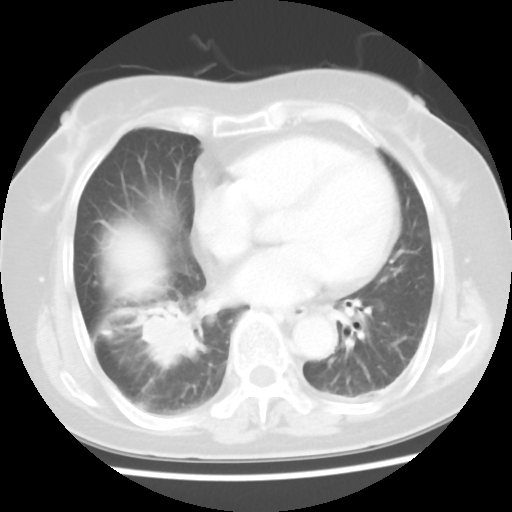
Chest CT, one axial slice; slice 17 of 45 in the series (ordered by position); reconstruction kernel STANDARD; lung window (W 1500 / L -600 HU); 5 mm slice thickness; 512 × 512 image matrix, field of view 312 × 312 mm. Patient: female, 65 years. Case-level facts recorded for this patient, not image findings: clinical TNM (as recorded): T2 N3 M0.
Structures marked on this image (bounding box drawn by a radiologist):
- lung tumour (recorded histology: adenocarcinoma): bounding box [x1, y1, x2, y2] px = [137, 312, 206, 385]